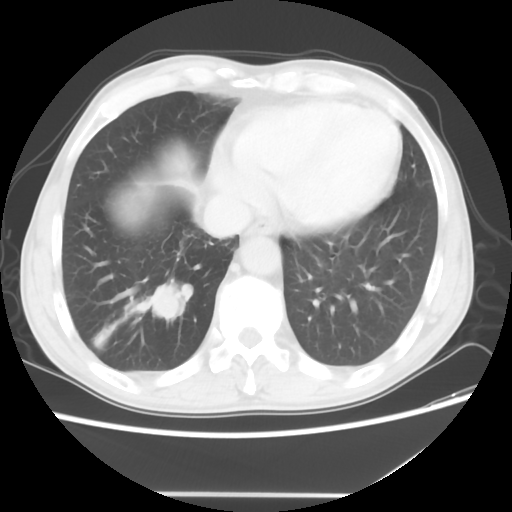
Chest CT, one axial slice. Slice 14 of 56 in the series (ordered by position). 120 kVp. Lung window (W 1500 / L -600 HU). 5 mm slice thickness. 512 × 512 image matrix, field of view 344 × 344 mm. Patient: male, 65 years. From the clinical record (not read from this slice): clinical TNM (as recorded): T1c N3 M0.
Structures marked on this image (bounding box drawn by a radiologist):
- lung tumour (recorded histology: small cell carcinoma): bounding box <137,276,198,331> (left, top, right, bottom; pixels)